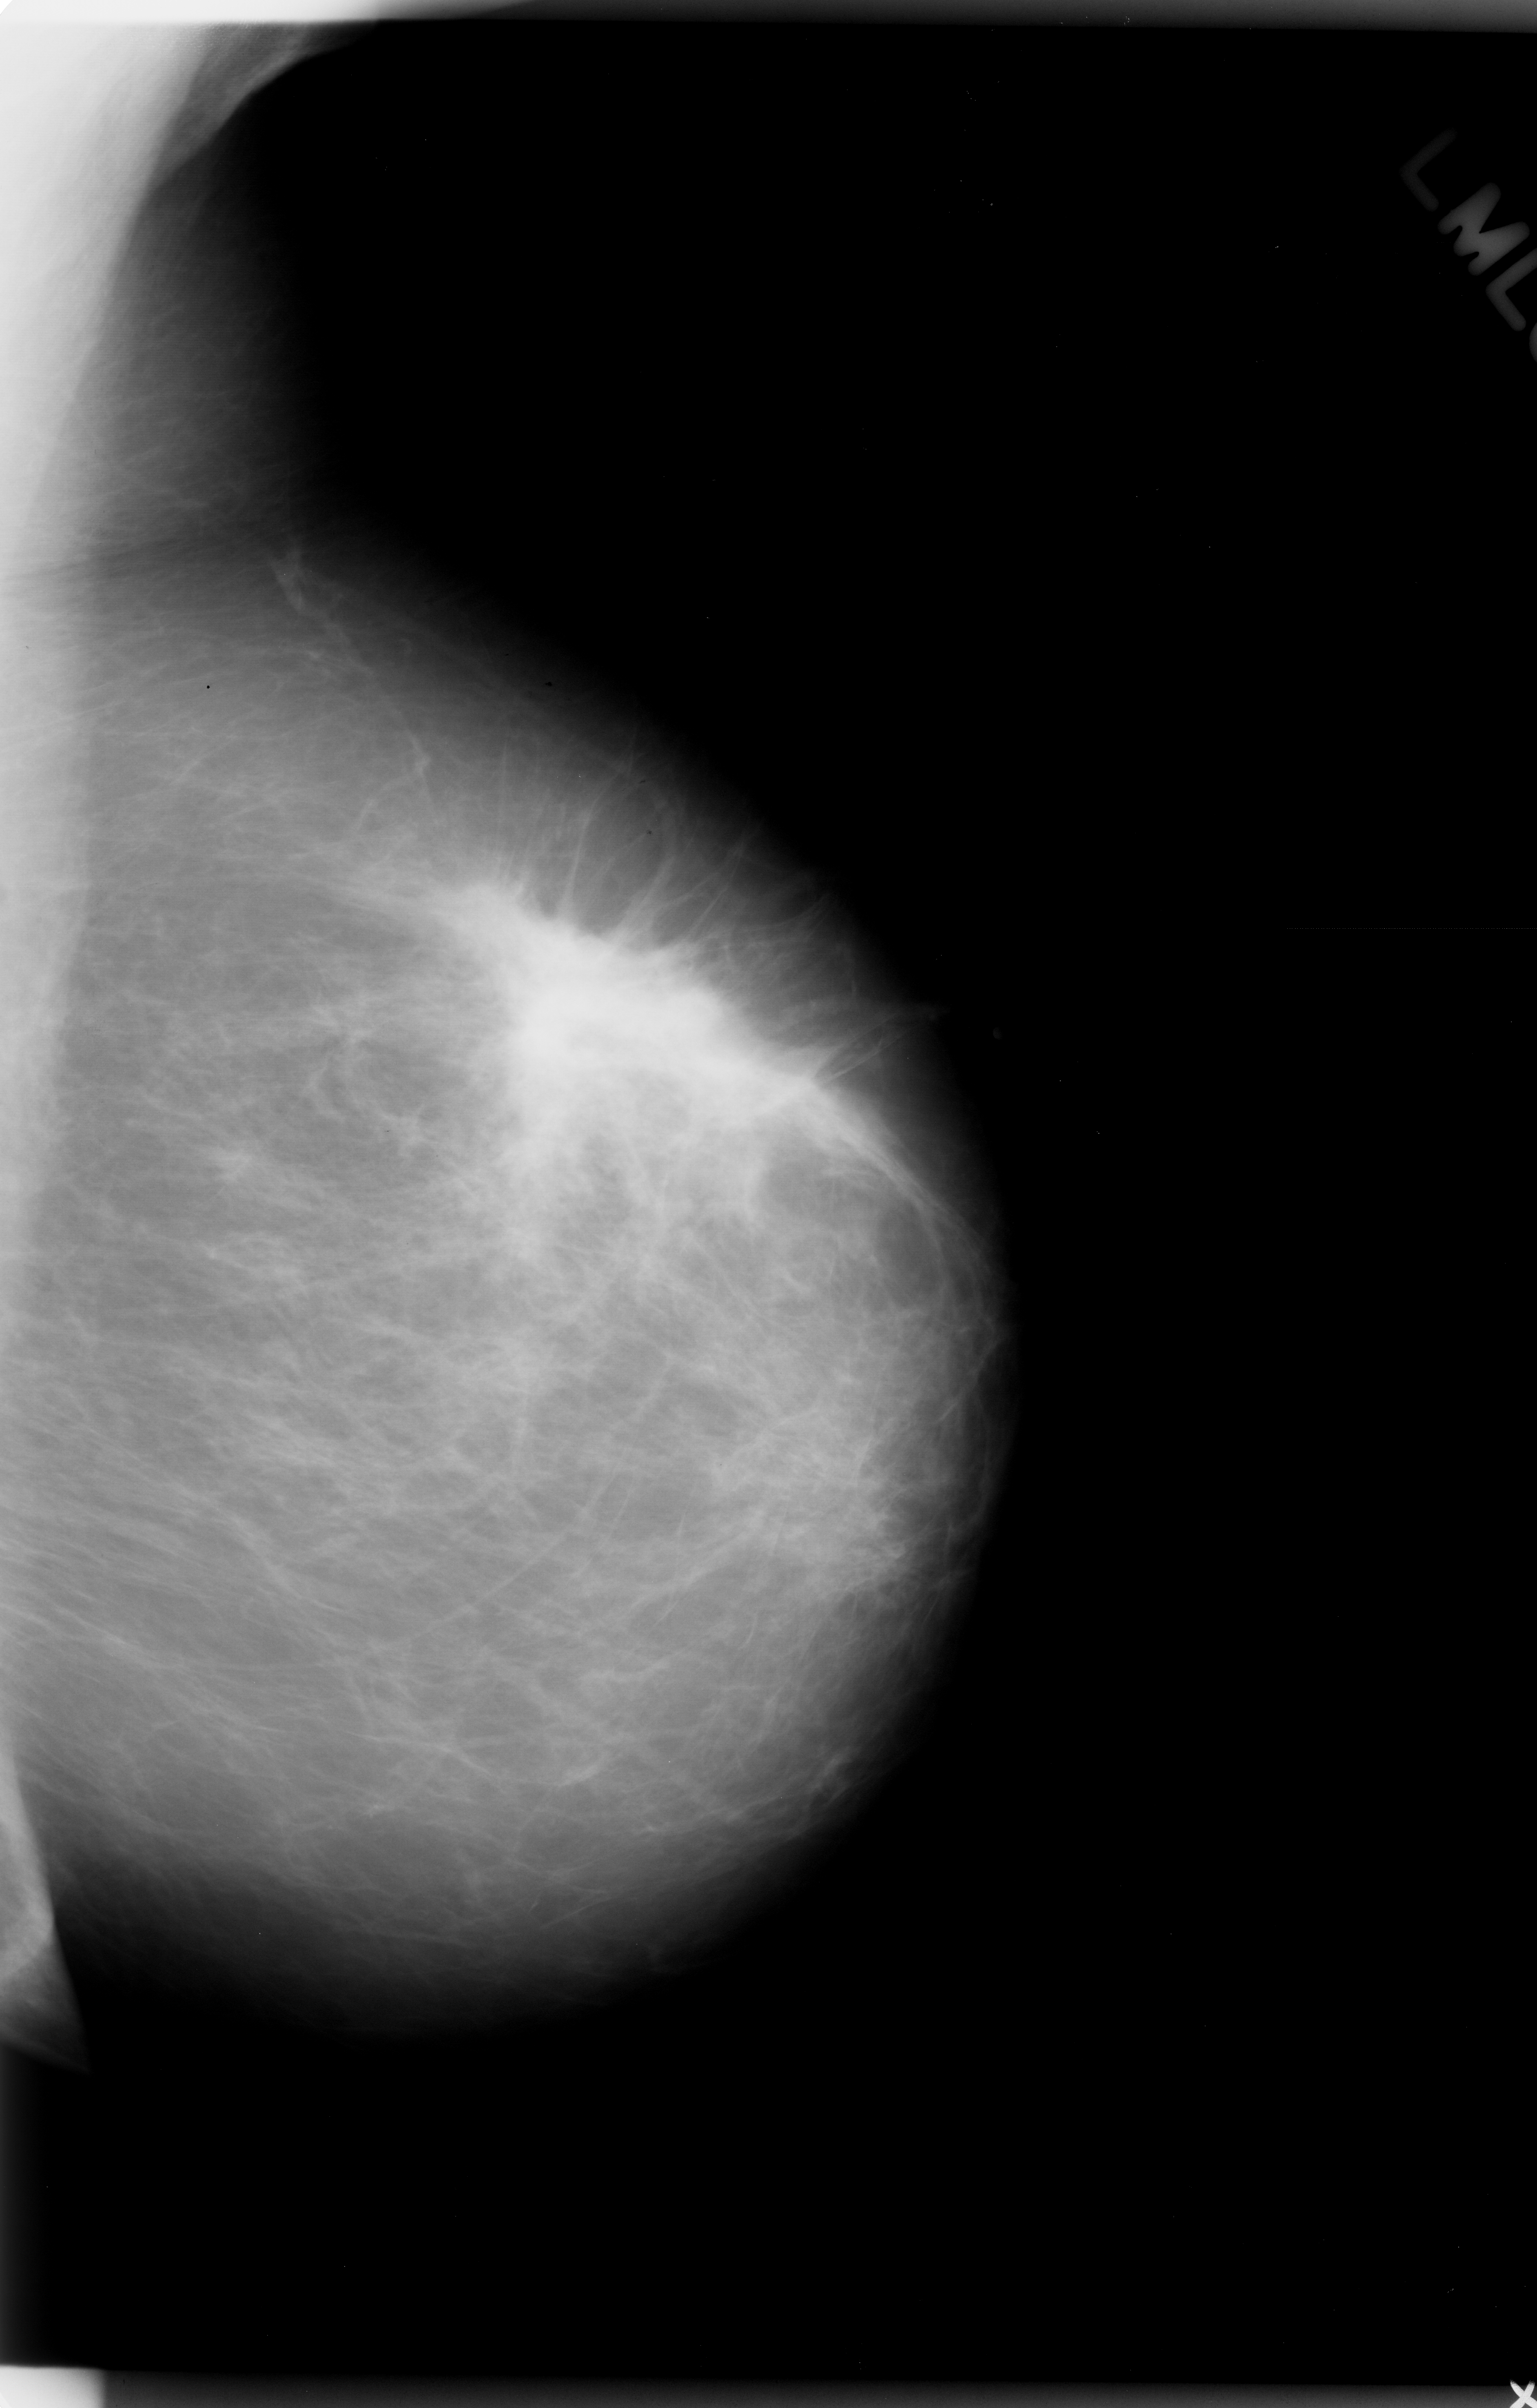
Digitized screen-film mammogram; left breast; mediolateral oblique (MLO) view; breast composition: almost entirely fatty (BI-RADS density category 1 of 4).
Finding: mass, shape irregular, margins spiculated; BI-RADS assessment category 5; pathology result (as recorded, not read from the image): malignant.